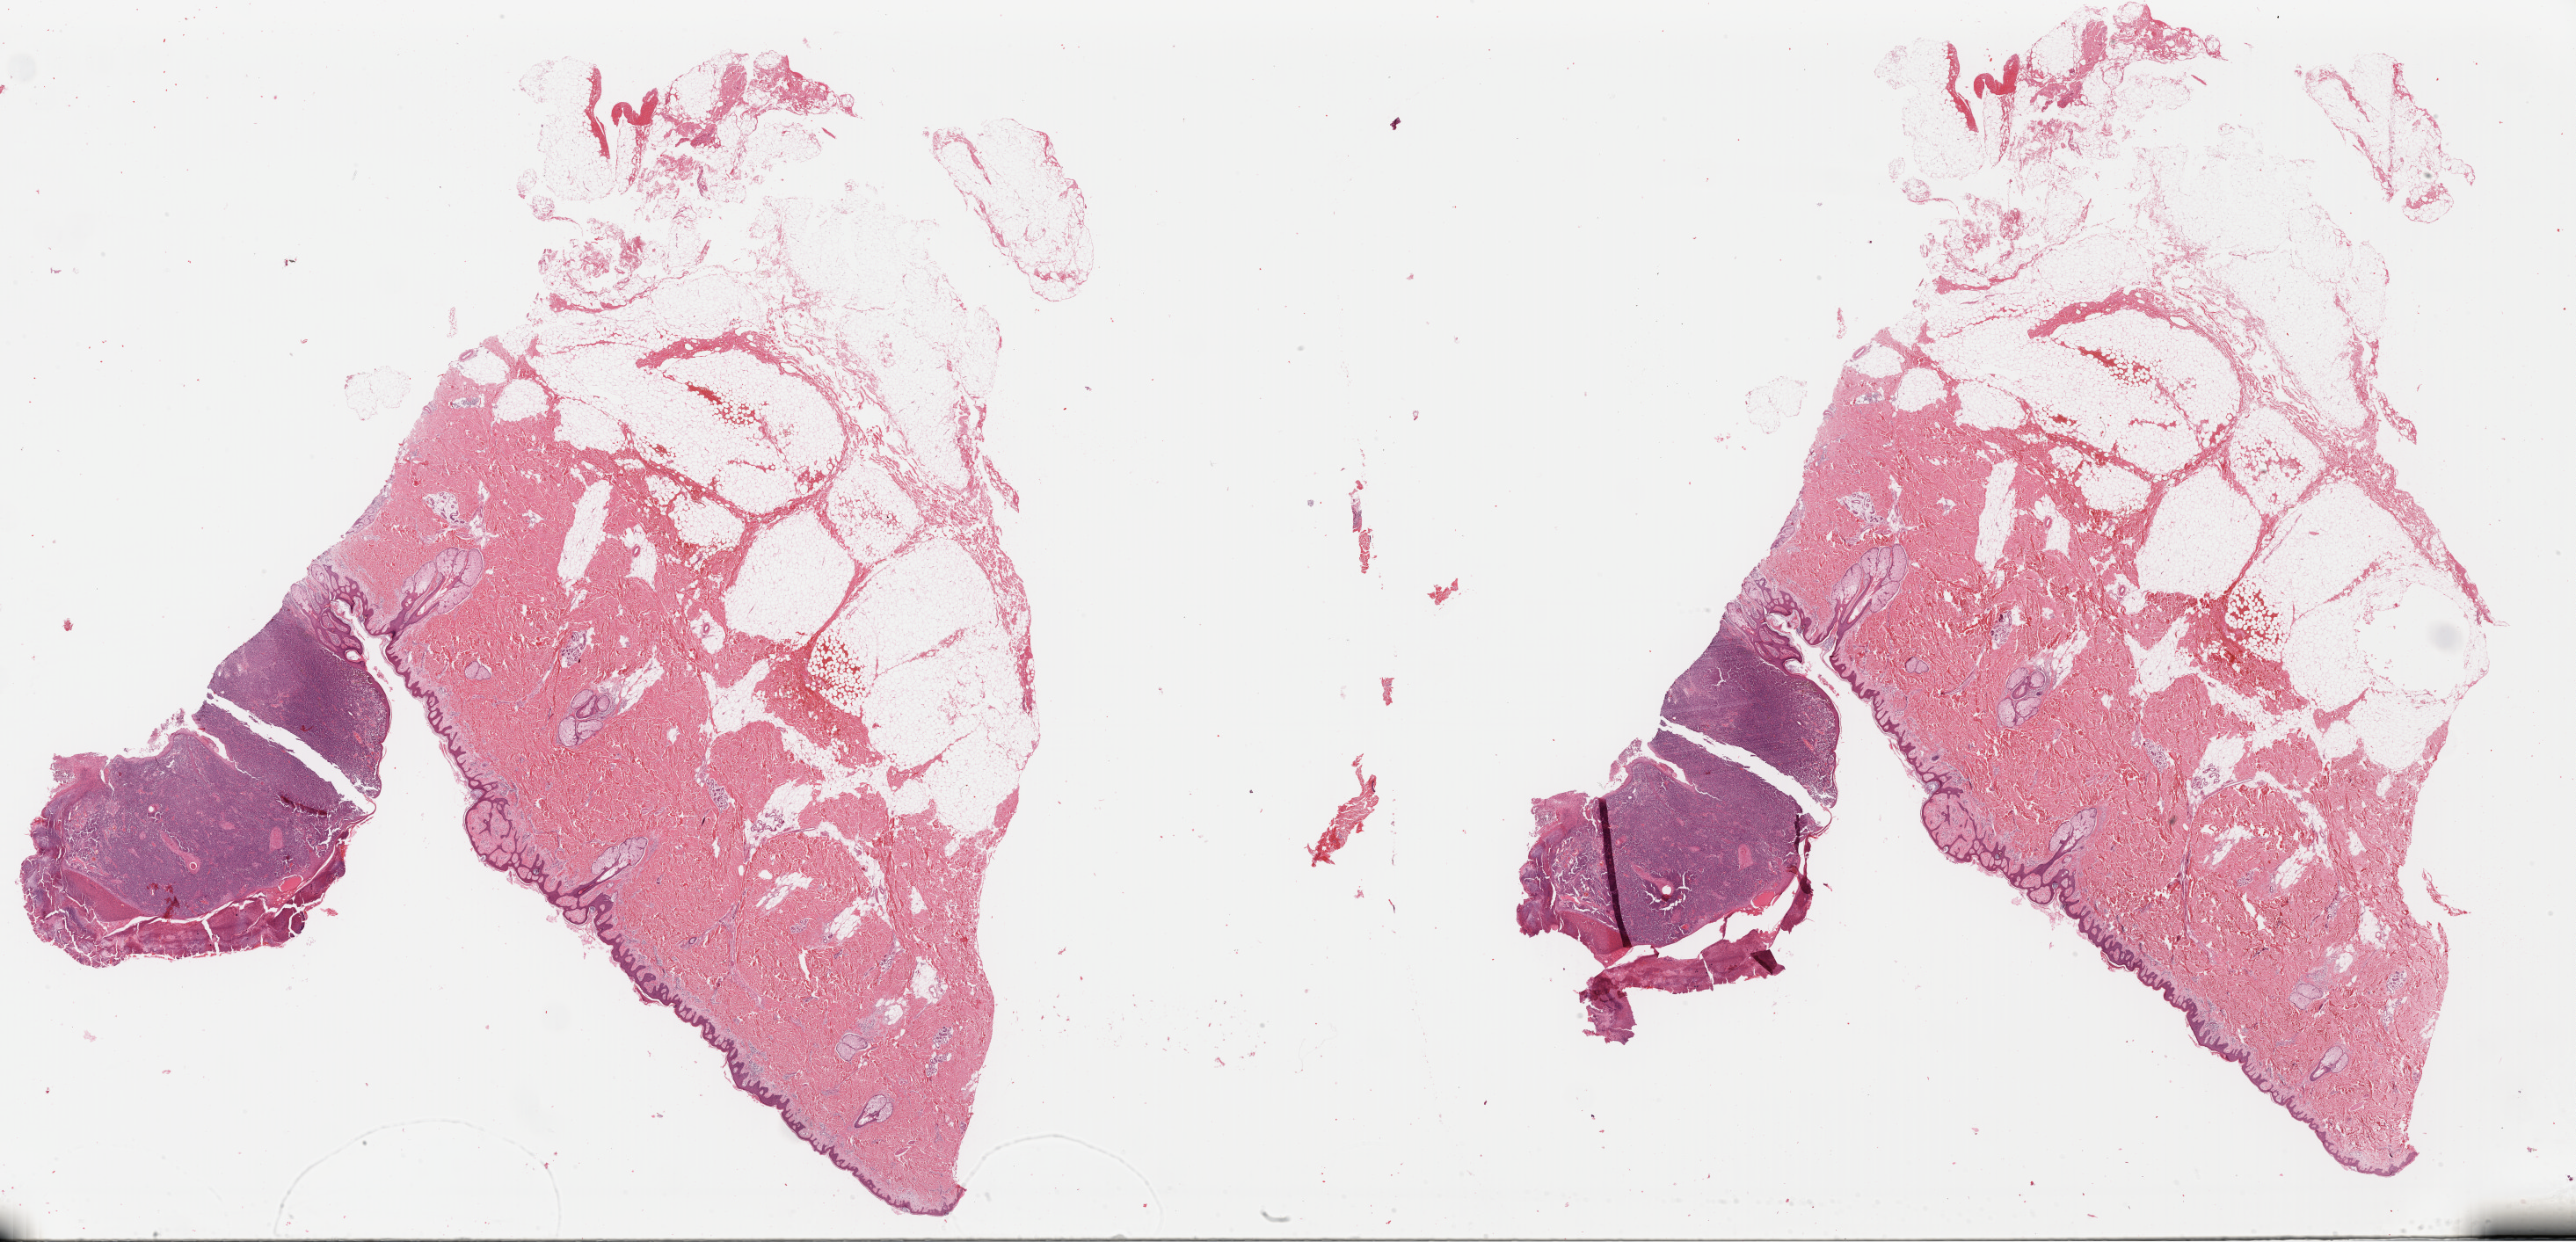
Digitized H&E tissue section (whole slide), whole scanned area (about 46.1 x 22.2 mm) shown as a low-resolution overview. Formalin-fixed paraffin-embedded (FFPE) diagnostic section. Sample: primary tumour, skin. Male patient; age at initial diagnosis 43 years.
* histologic diagnosis: Malignant melanoma, NOS
* AJCC pathologic stage: IIIA (5th edition)